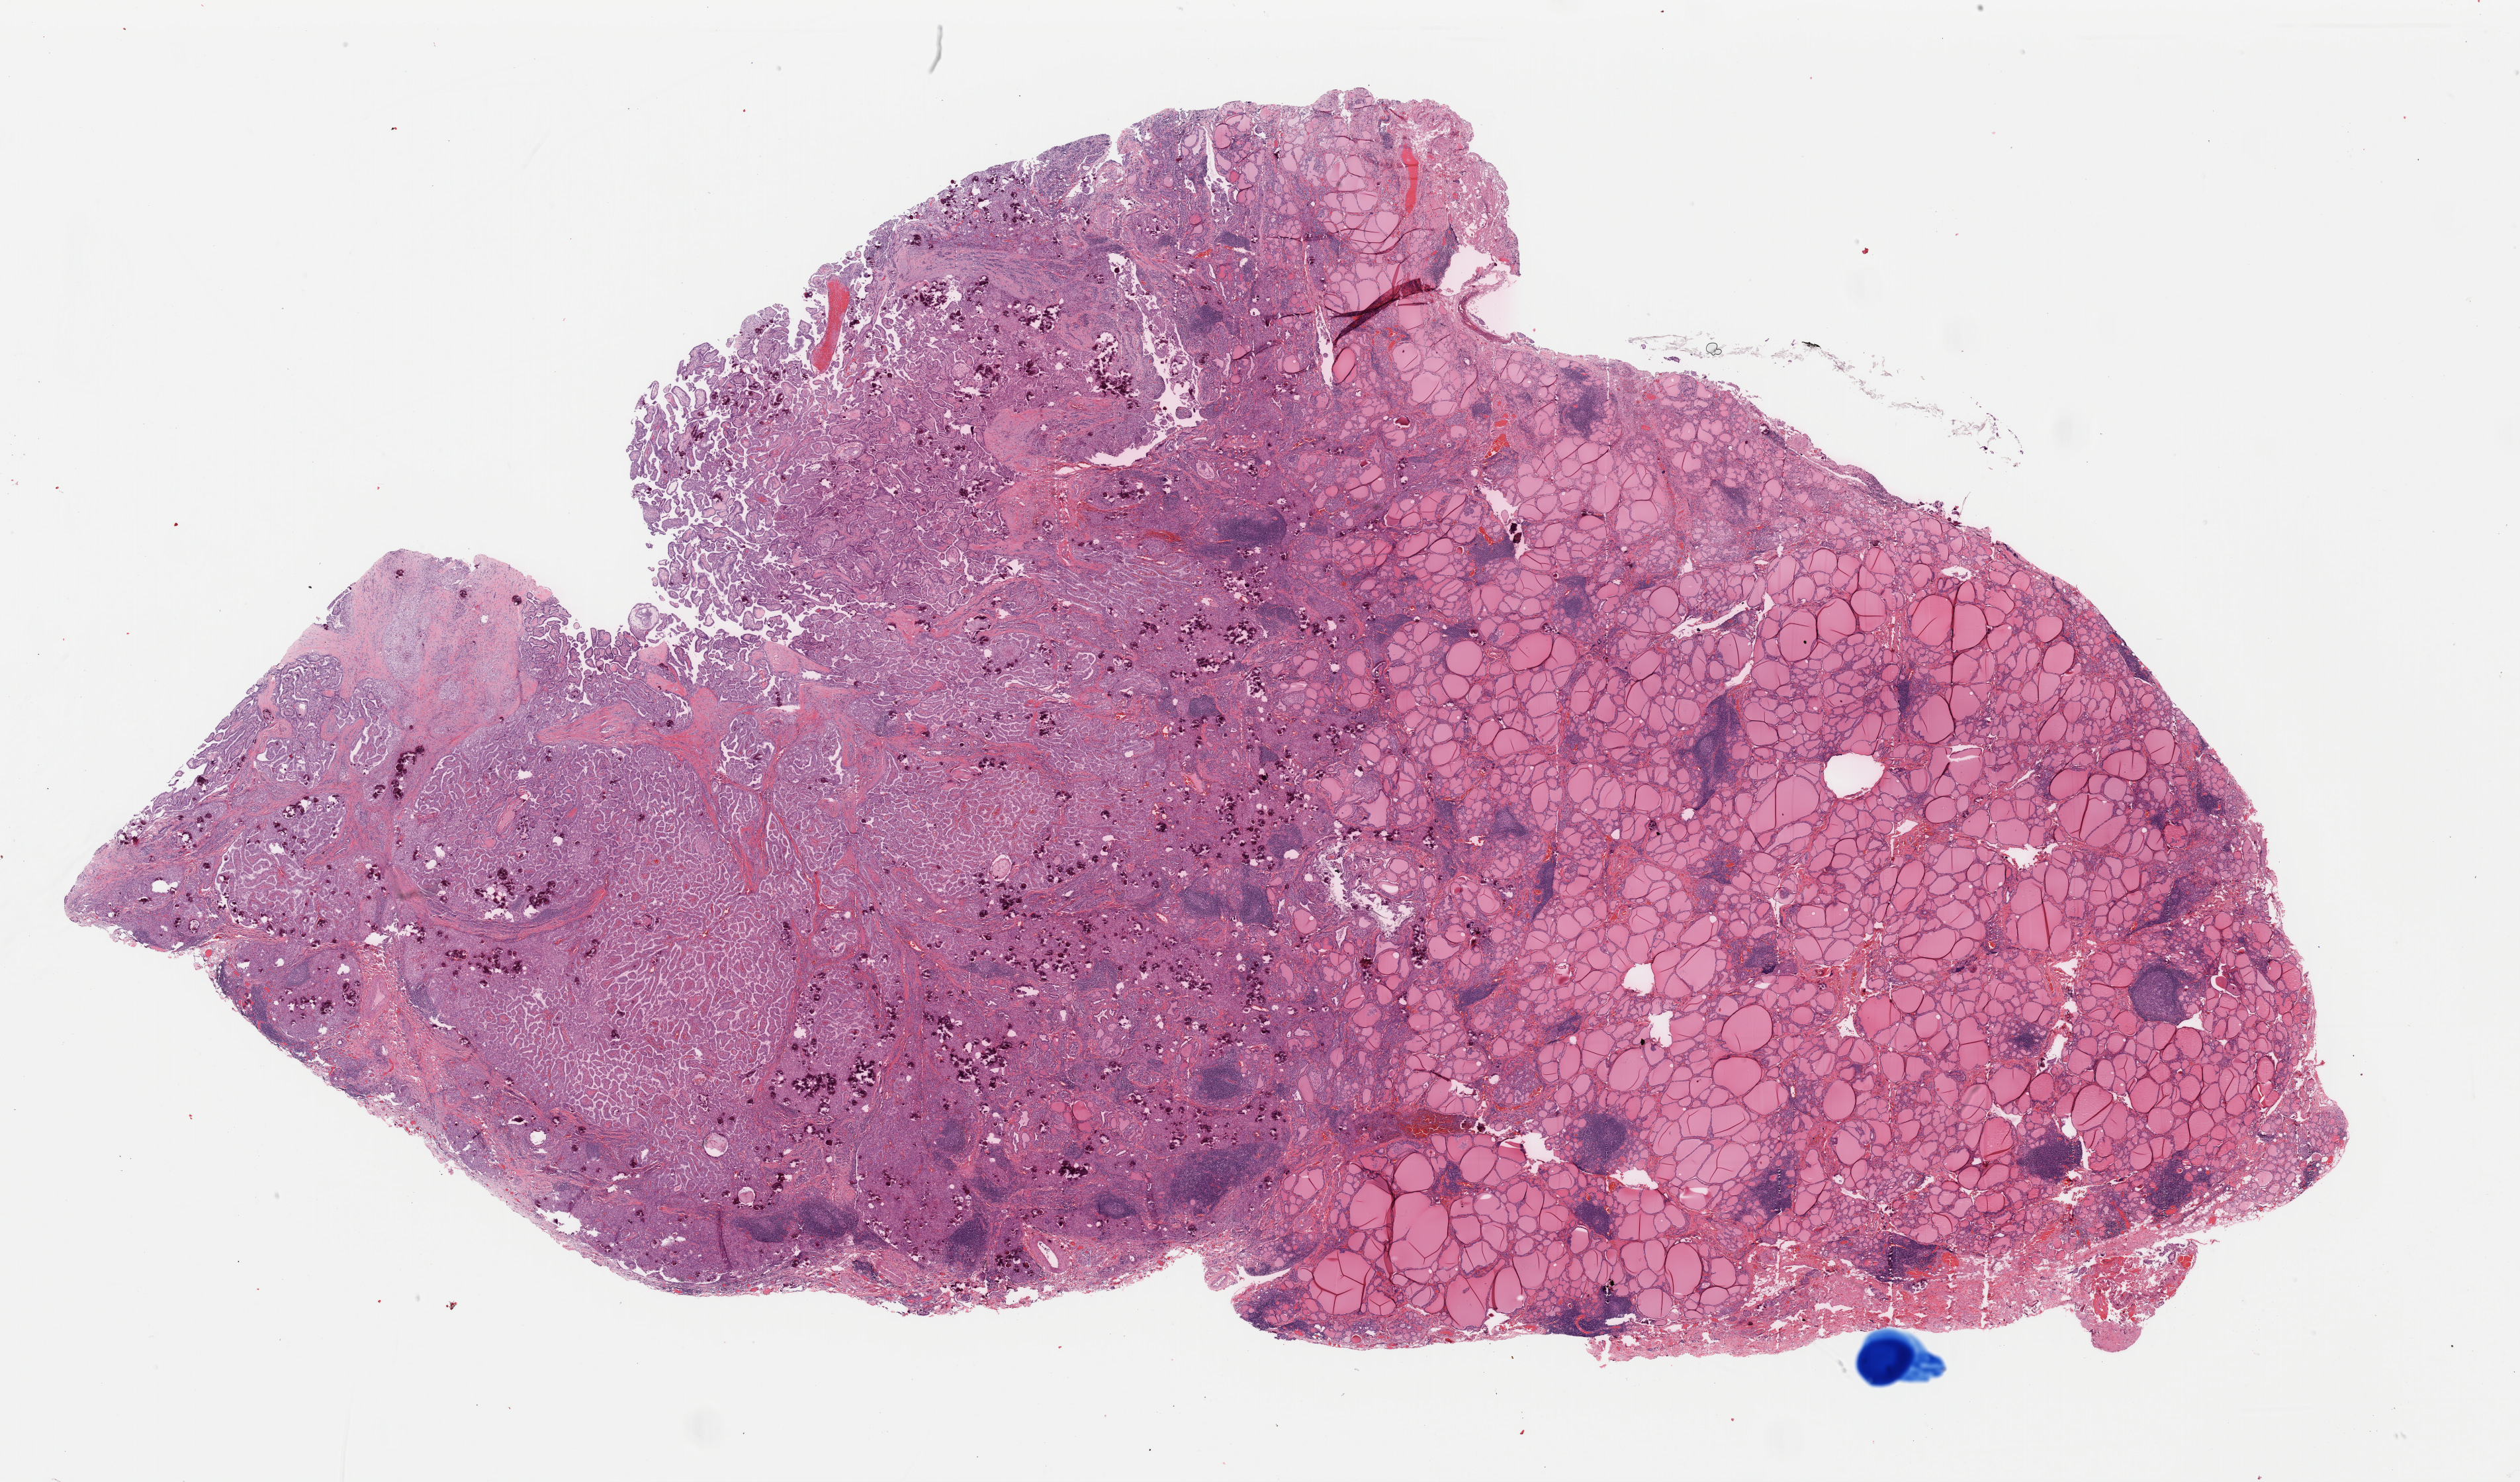
Whole-slide histology image, Hematoxylin and eosin (H&E) stained — low-resolution overview of the scanned area, about 30.1 x 17.7 mm (from a 40x scan), formalin-fixed paraffin-embedded (FFPE) diagnostic section, primary tumour sample from the thyroid. Male, age 19 years at initial diagnosis.
• diagnosis: Papillary adenocarcinoma, NOS (thyroid gland)
• laterality: right
• AJCC pathologic stage: I (6th edition)